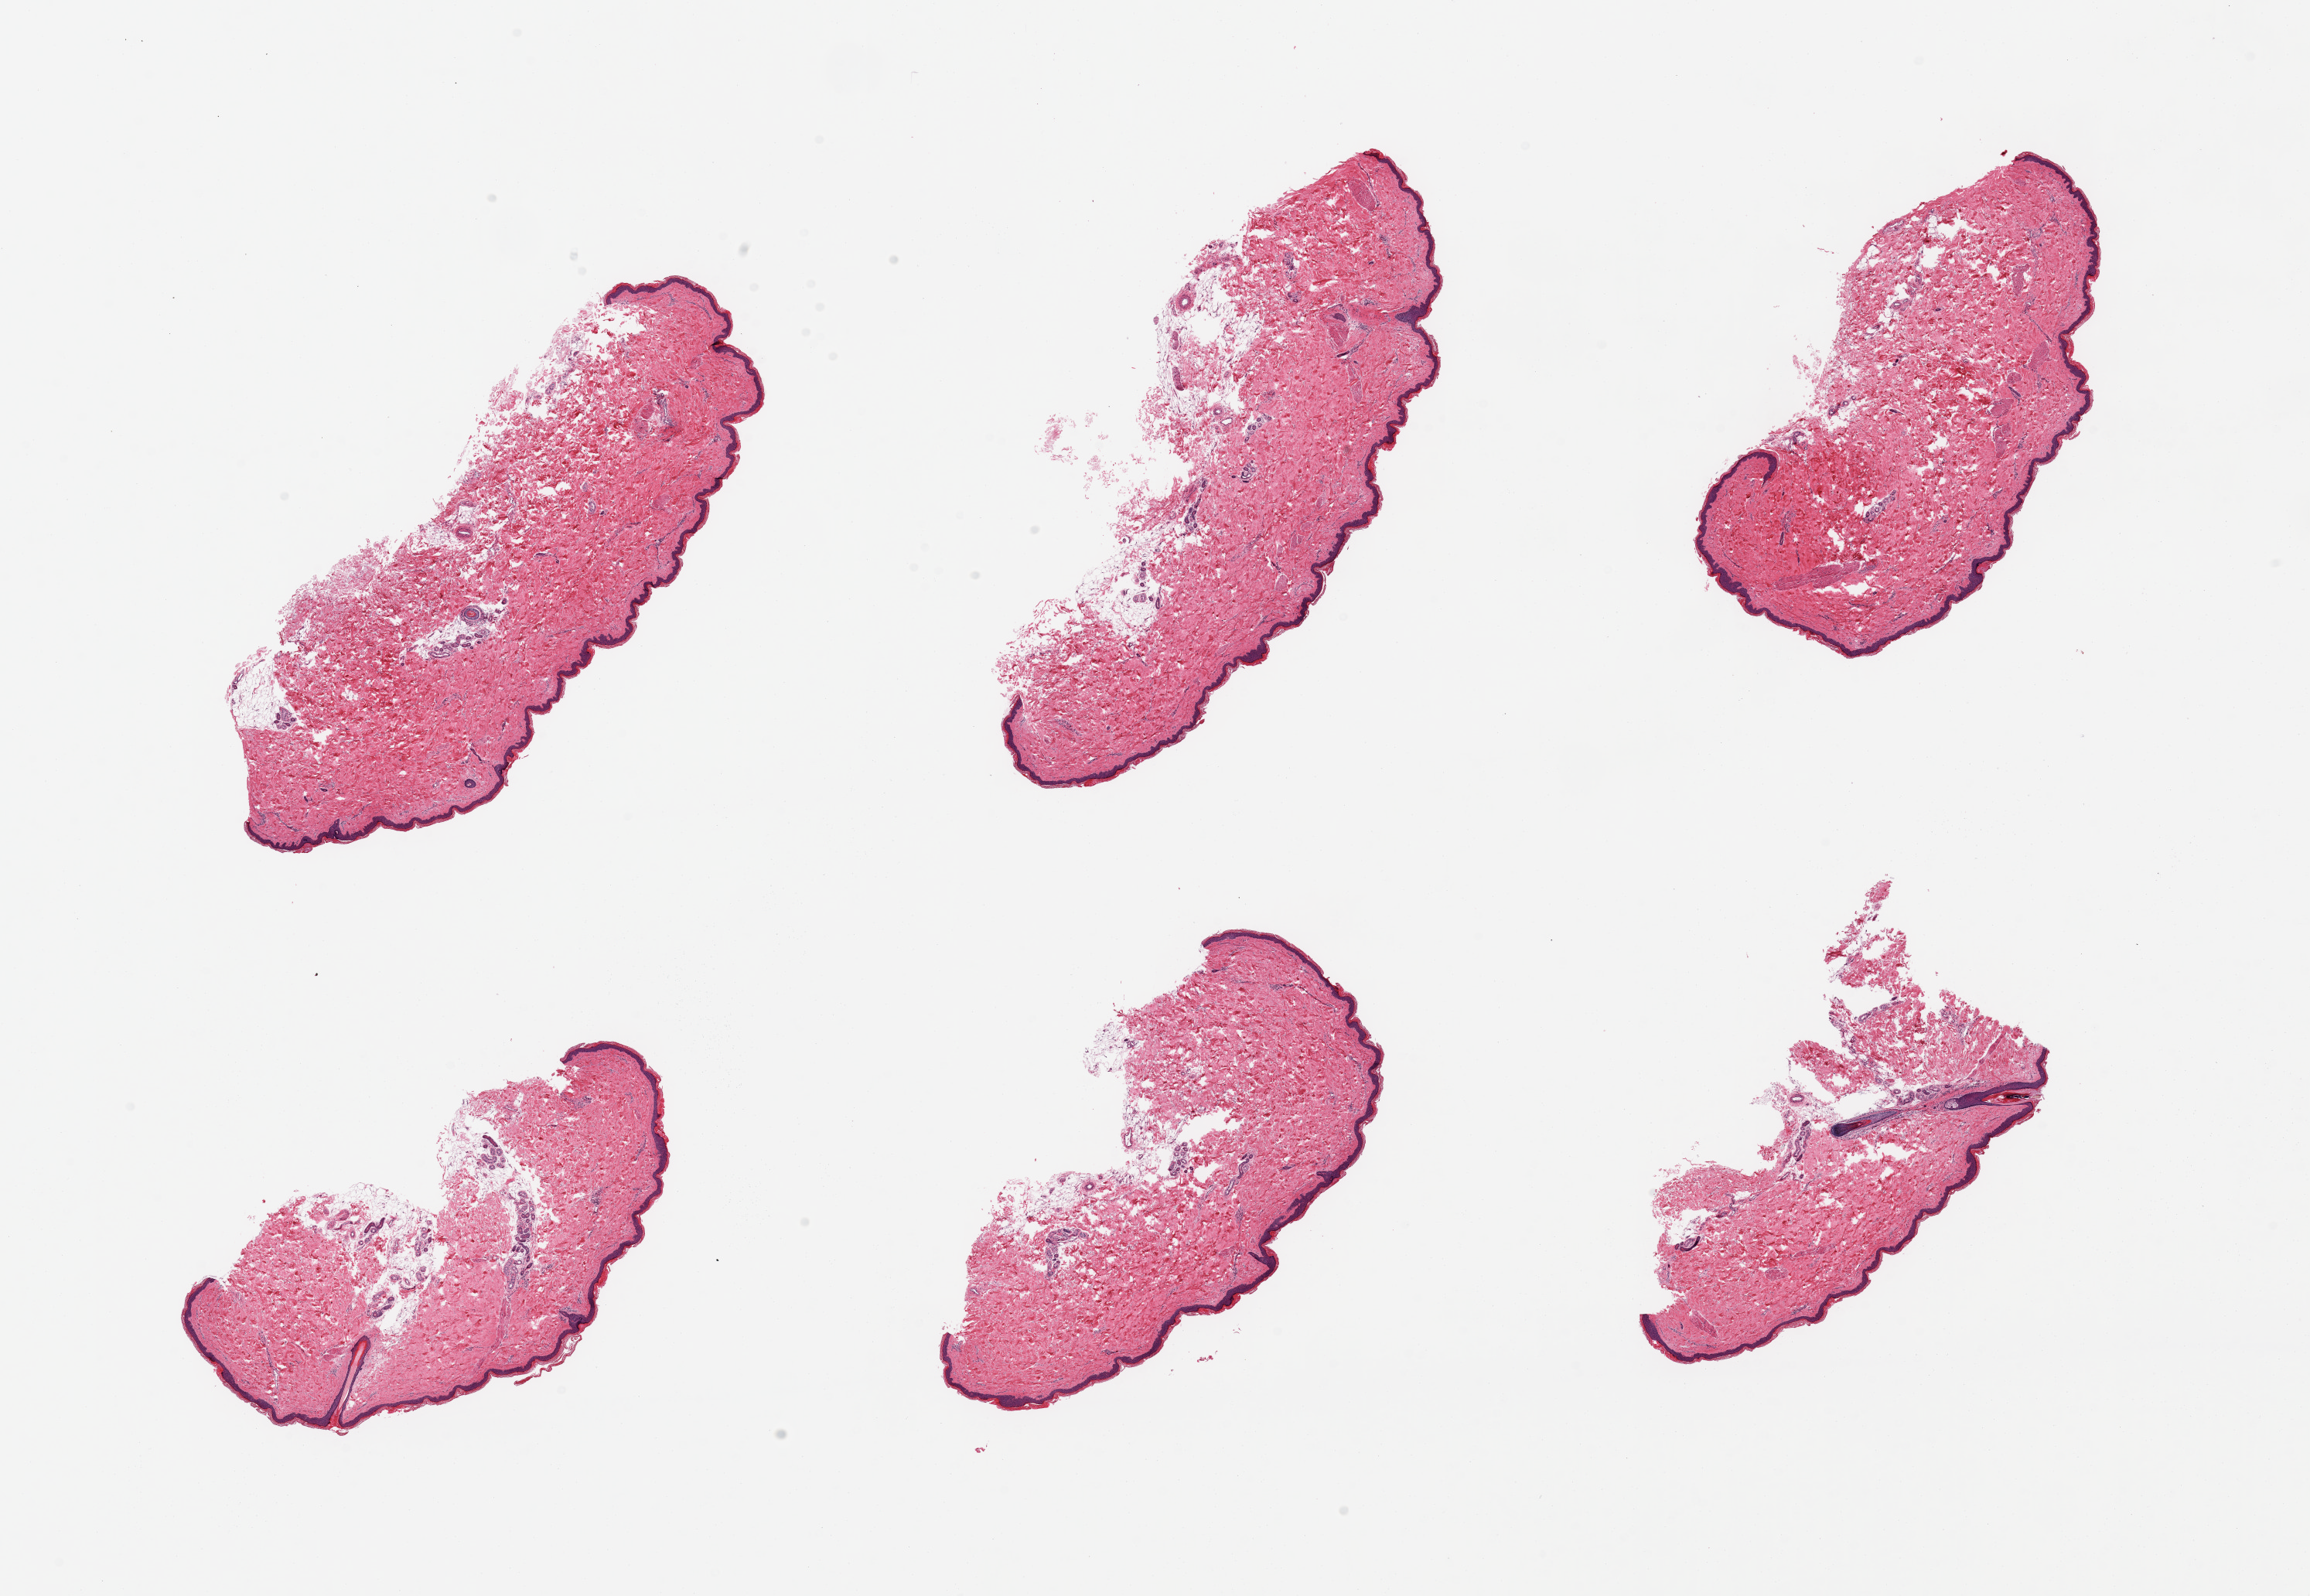
Haematoxylin and eosin whole-slide image, brightfield — low-resolution overview of the scanned area, about 23.6 x 16.3 mm; PAXgene-fixed paraffin-embedded (PFPE) section; target tissue: skin of lower leg; donor tissue sample.
Review note (as recorded): 6 pieces, minimal dermal fat; squamous epithelium is ~60 microns.